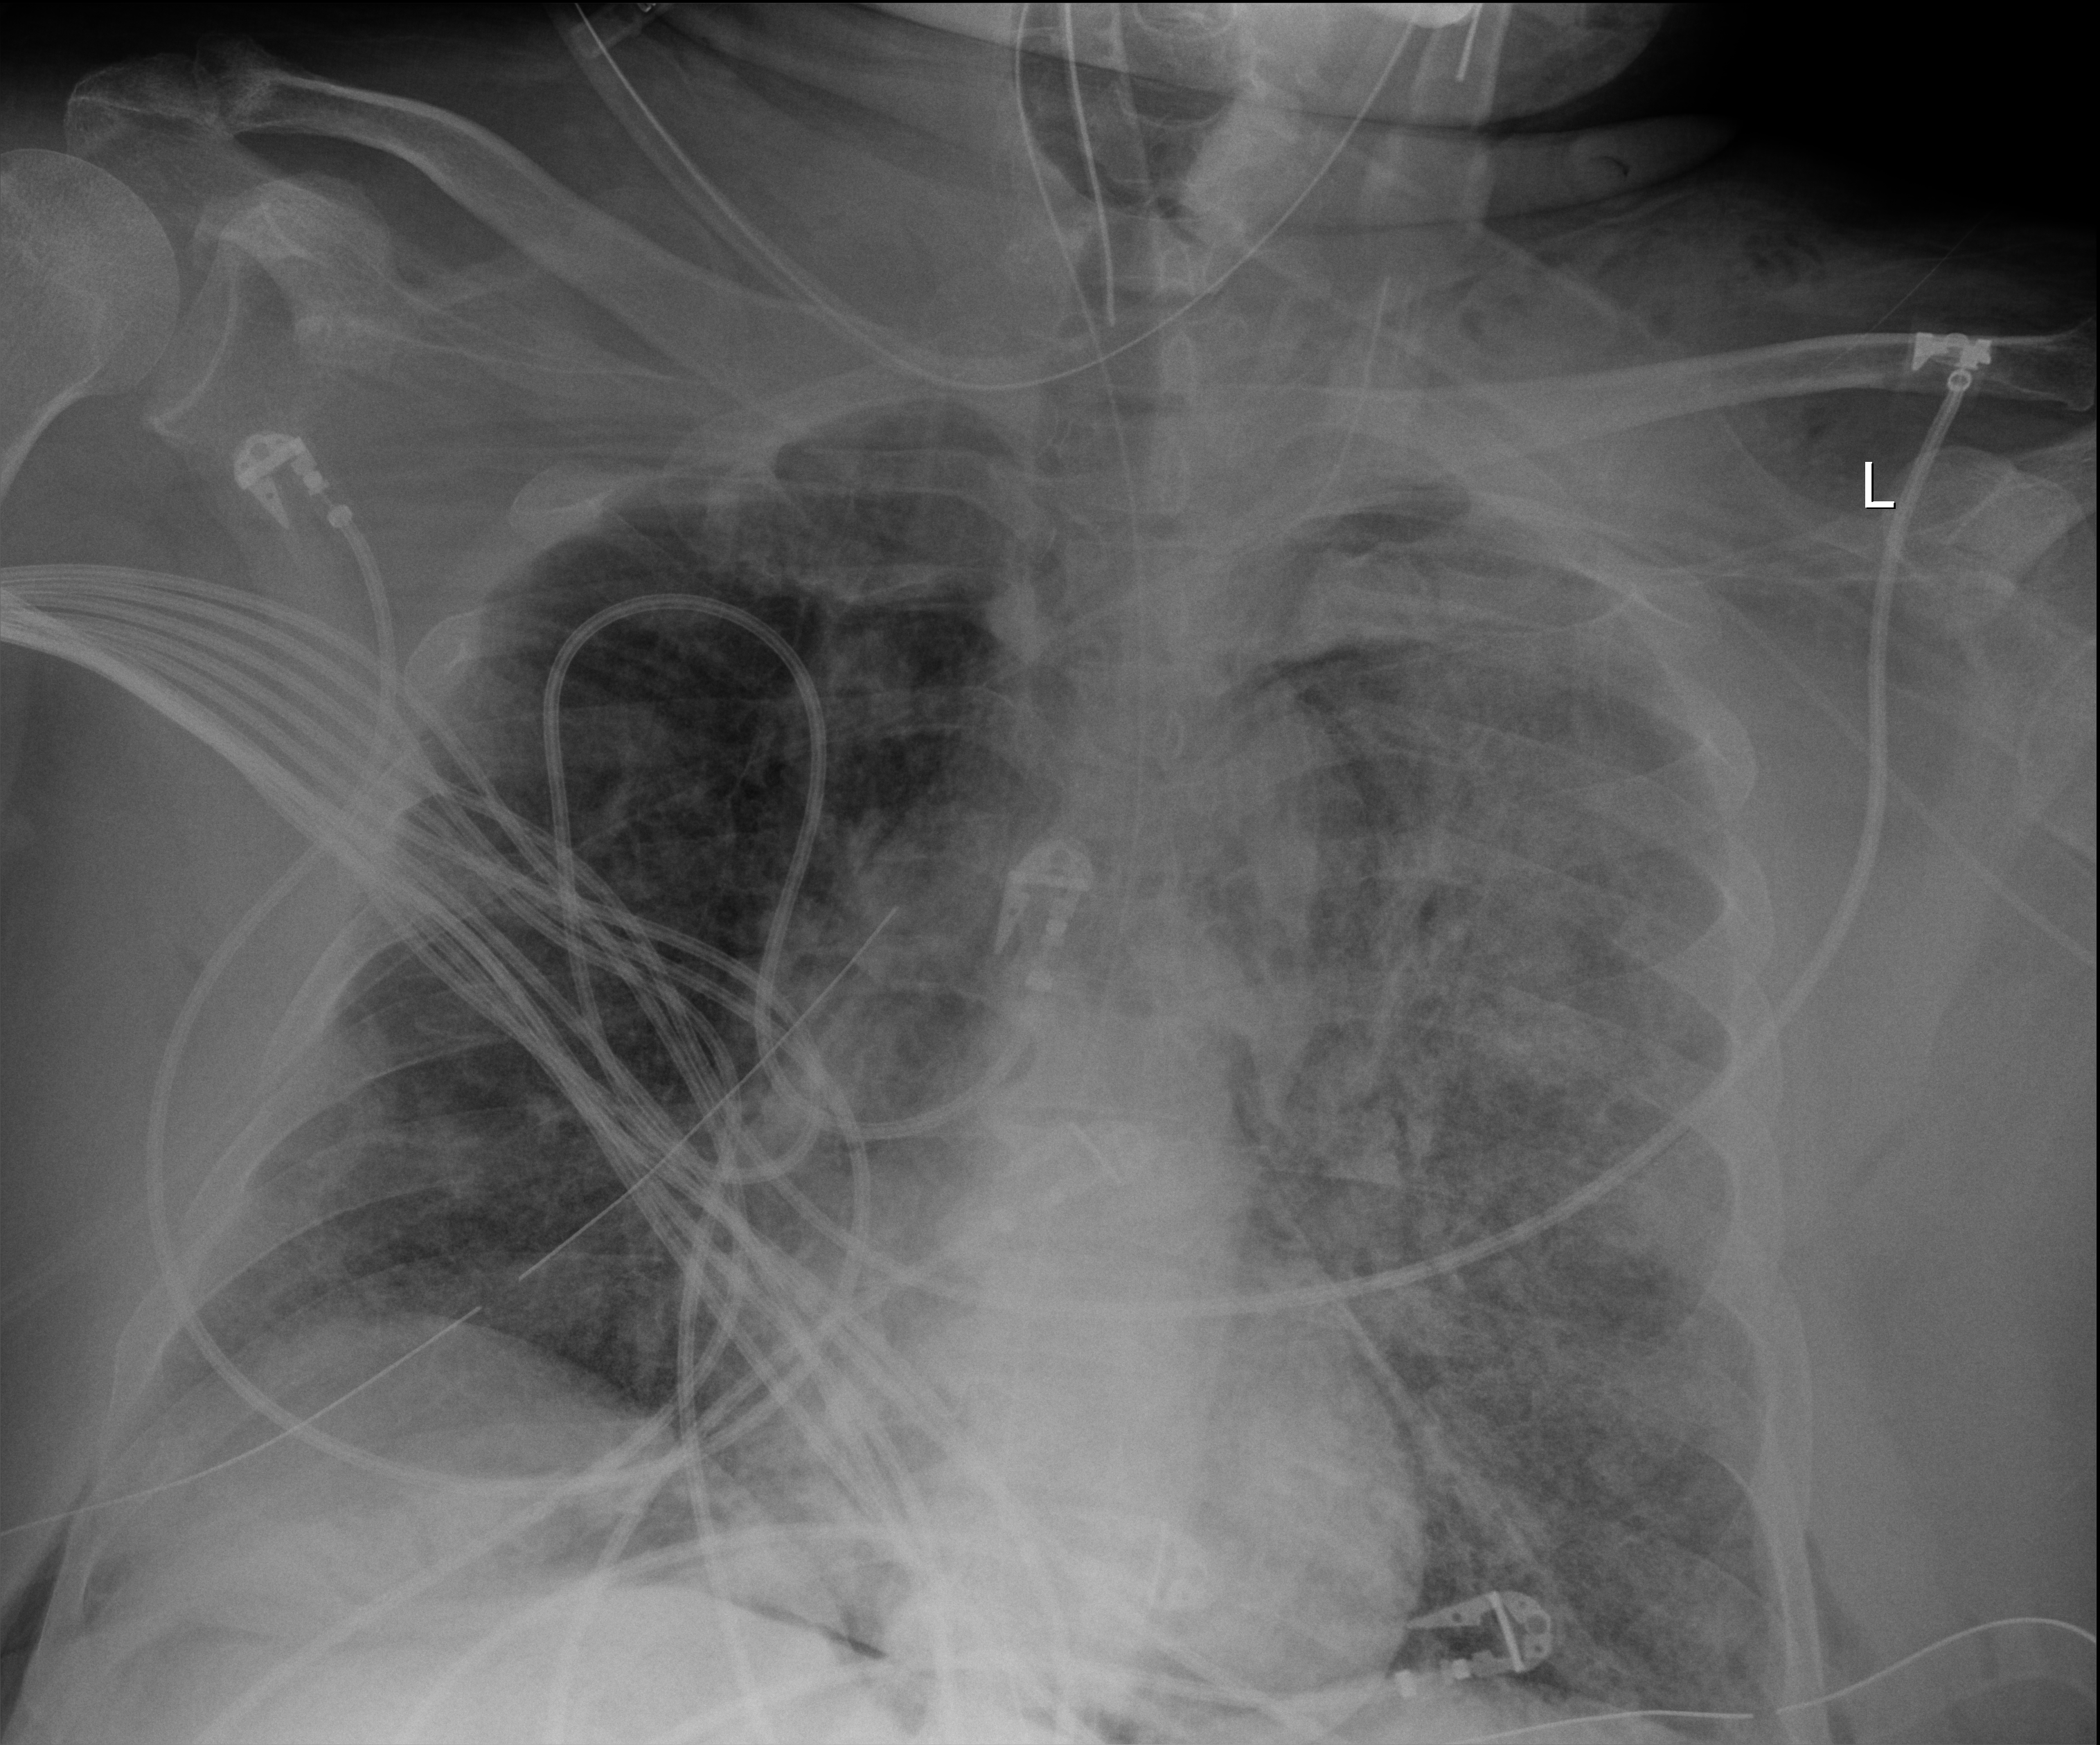
Bedside chest radiograph (digital radiography); anteroposterior (AP) projection. Patient hospitalised with COVID-19, aged 18–59 years.
From the hospital-stay record, not from the radiograph (when in the stay this image was taken is not recorded):
- length of hospital stay: 28 days